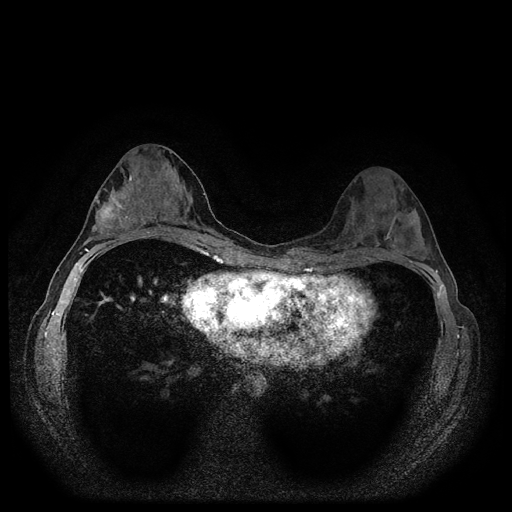
Breast MRI (dynamic contrast-enhanced, multi-phase), one axial slice. Slice 53 of 116 in the series (ordered by position). Dynamic contrast-enhanced series, time point 2 of 5 at this slice position (early post-contrast). 1.5 T. TE 2.7 ms, TR 5.4 ms. 512 × 512 image matrix, field of view 320 × 320 mm. Patient: female, 29 years.
Outlined on this slice (semi-automatically segmented with operator editing):
- breast lesion (labelled 'tumour' in the annotation; benign lesions carry a separate 'benign' label): bounding box [x1, y1, x2, y2] px = [95, 190, 129, 228]